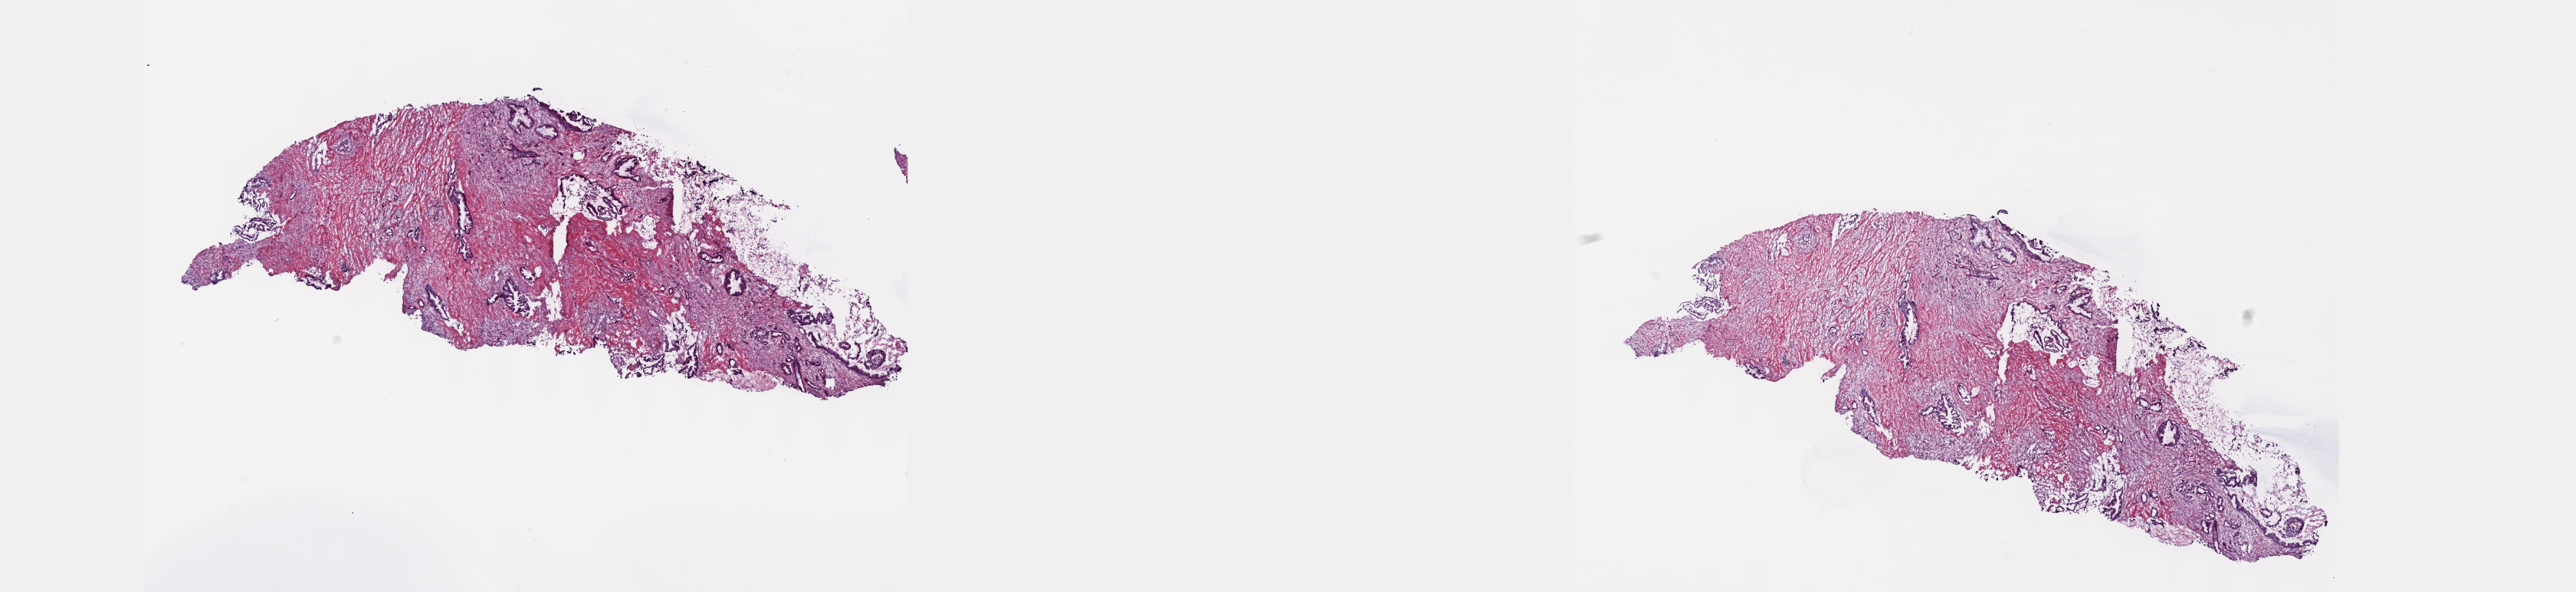
Whole-slide histology image, Hematoxylin and eosin (H&E) stained — shown as a low-resolution overview of the whole scanned area (about 27.2 x 6.2 mm, from a 40x scan), frozen section from the top of the tissue portion, primary tumour sample from the pancreas. Patient: male, age at initial diagnosis 81 years. Histologic grade: G1 (well differentiated). Pathologist review of this section (percent, as recorded): tumour cells 30%, tumour nuclei 90%, normal cells 5%, stromal cells 65%, necrosis 0%. Infiltration values recorded for this section: lymphocyte infiltration 2%, monocyte infiltration 4%, neutrophil infiltration 0%.
AJCC pathologic stage: IB (7th edition). Lymph nodes positive (case pathology): 0 of 5 examined. Diagnosis: Infiltrating duct carcinoma, NOS (tail of pancreas).